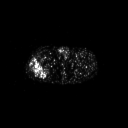
FDG PET of an extremity soft-tissue mass (from a PET/CT study), one axial slice; 3.27 mm slice thickness; 128 × 128 image matrix. Male patient, age 43 years. Case-level facts recorded for this patient, not image findings: histological type: poorly differentiated synovial sarcoma; grade: high; site of the primary tumour: right buttock.
Annotated regions visible in this slice (expert contour drawn on MRI and transferred to this co-registered scan by the dataset authors):
- gross tumour volume including surrounding oedema: bounding box [x1, y1, x2, y2] px = [29, 59, 51, 78]
- gross tumour volume (mass): [29, 59, 48, 78]